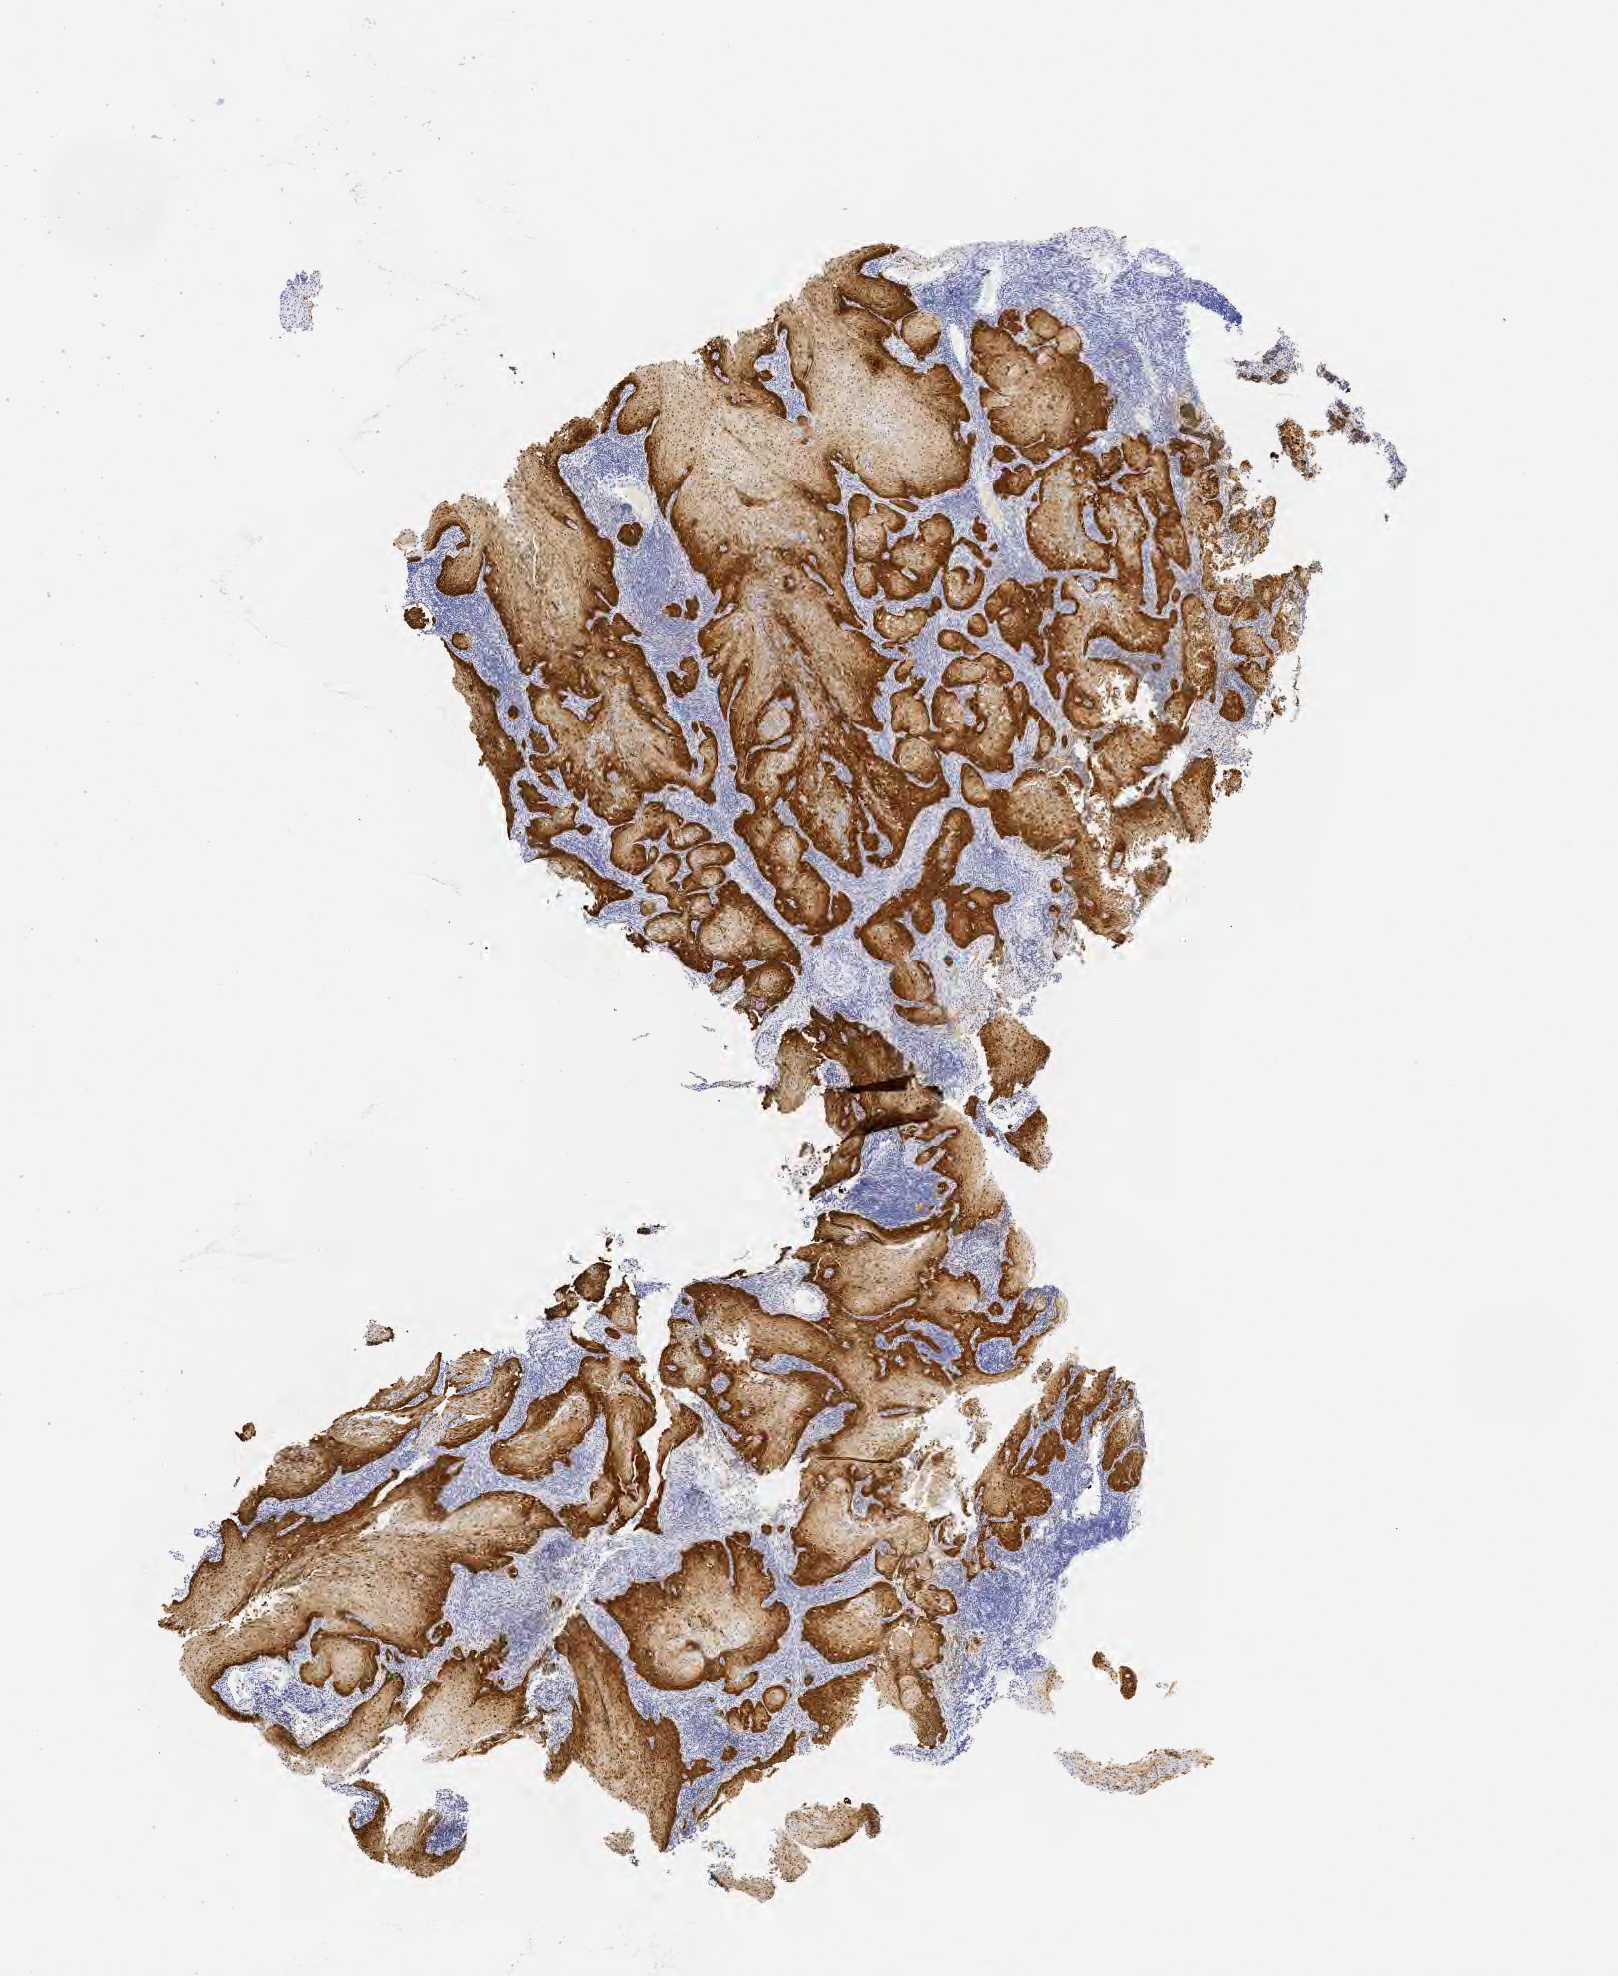
IHC for p16 (p16INK4a), whole-slide image, whole scanned area (about 6.5 x 8.0 mm) shown as a low-resolution overview. Tumor tissue. Anatomic site: cervix. Patient: female, aged 57.
Histologic diagnosis: Squamous cell carcinoma, large cell, nonkeratinizing, NOS.